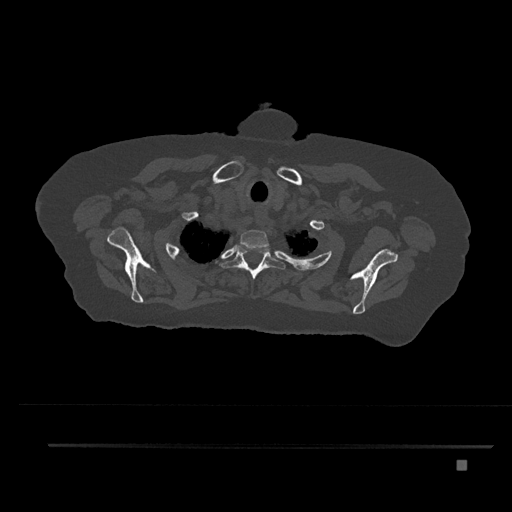
CT including the spine, one axial slice; slice 677 of 797 in the series (ordered by position); reconstruction kernel Br40s/3; 120 kVp; bone window (W 1800 / L 400 HU); 0.5 mm slice thickness; 512 × 512 image matrix, field of view 437 × 437 mm. Patient: female, 76 years. Case-level facts recorded for this patient, not image findings: primary cancer: lung; vertebrae with lytic lesions (as recorded): T11, L3.
Outlined on this slice (semi-automatically segmented with operator editing):
- T1 vertebra: bounding box [x1, y1, x2, y2] px = [240, 230, 269, 249]
- T2 vertebra: [220, 244, 289, 279]